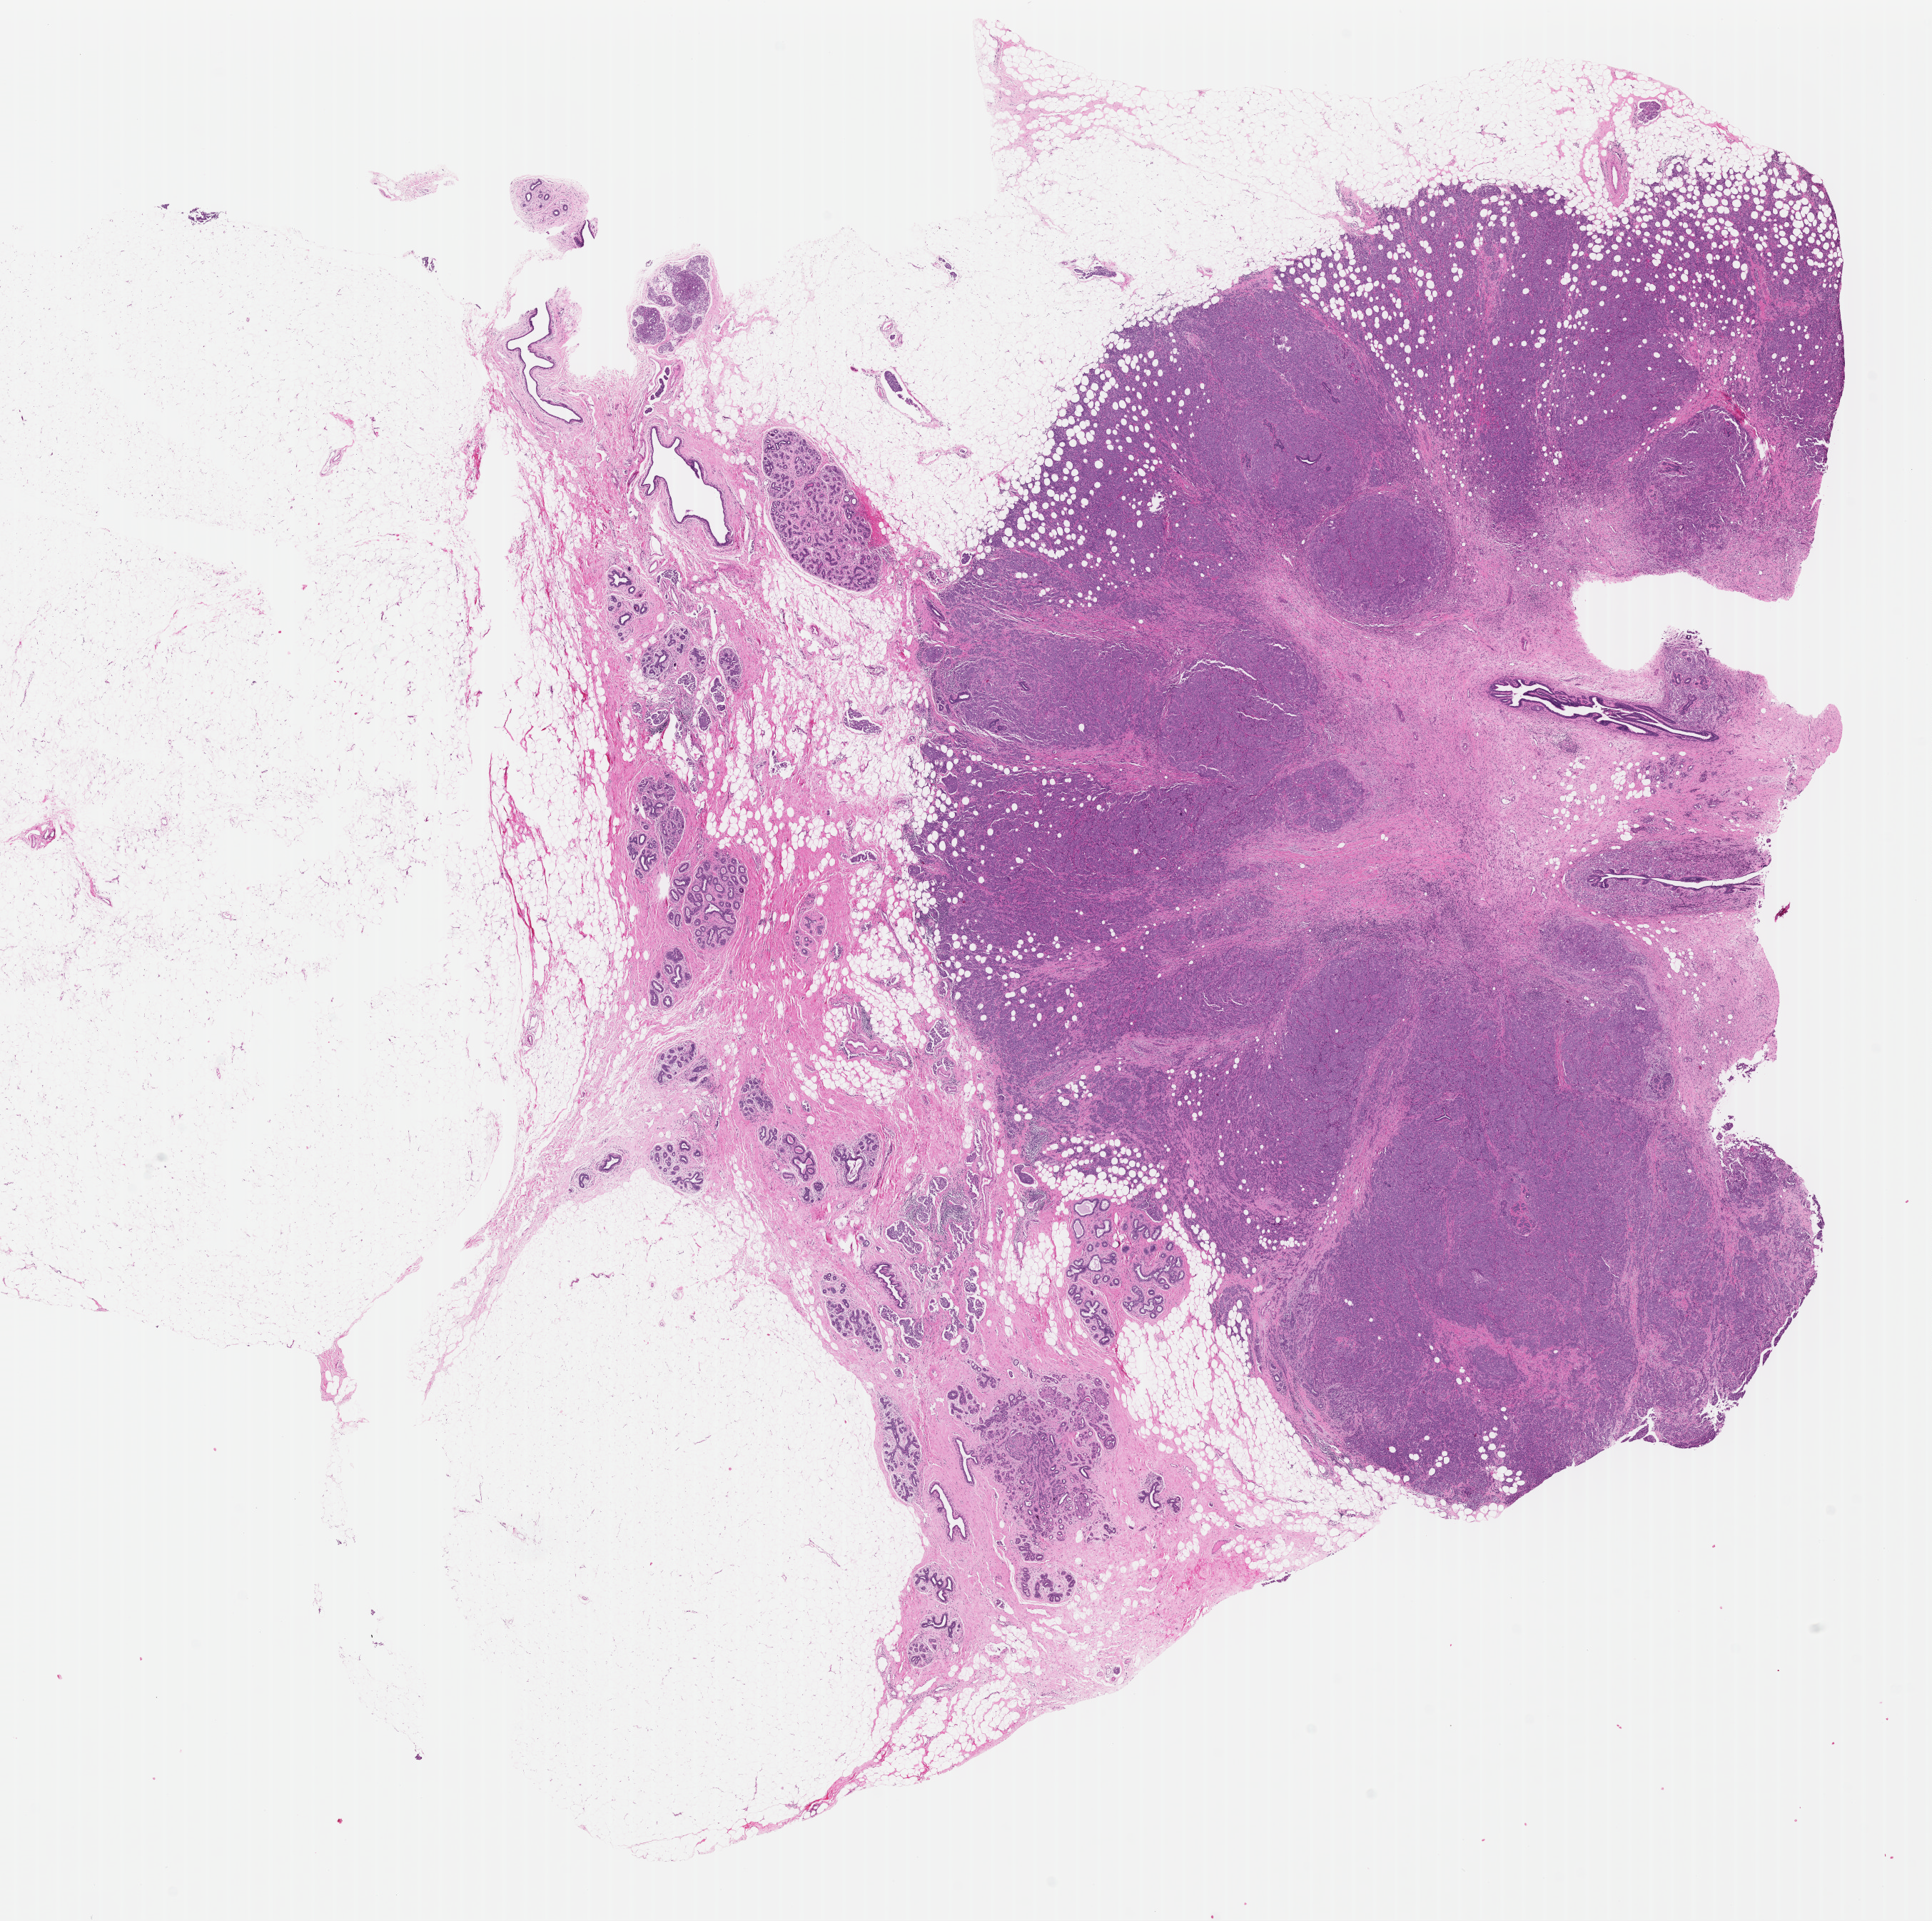
H&E-stained whole-slide image, whole scanned area (about 21.3 x 21.2 mm) shown as a low-resolution overview. FFPE section. Breast, primary tumour sample. Female, age 42 years at initial diagnosis.
Pathologic diagnosis: Infiltrating duct carcinoma, NOS.